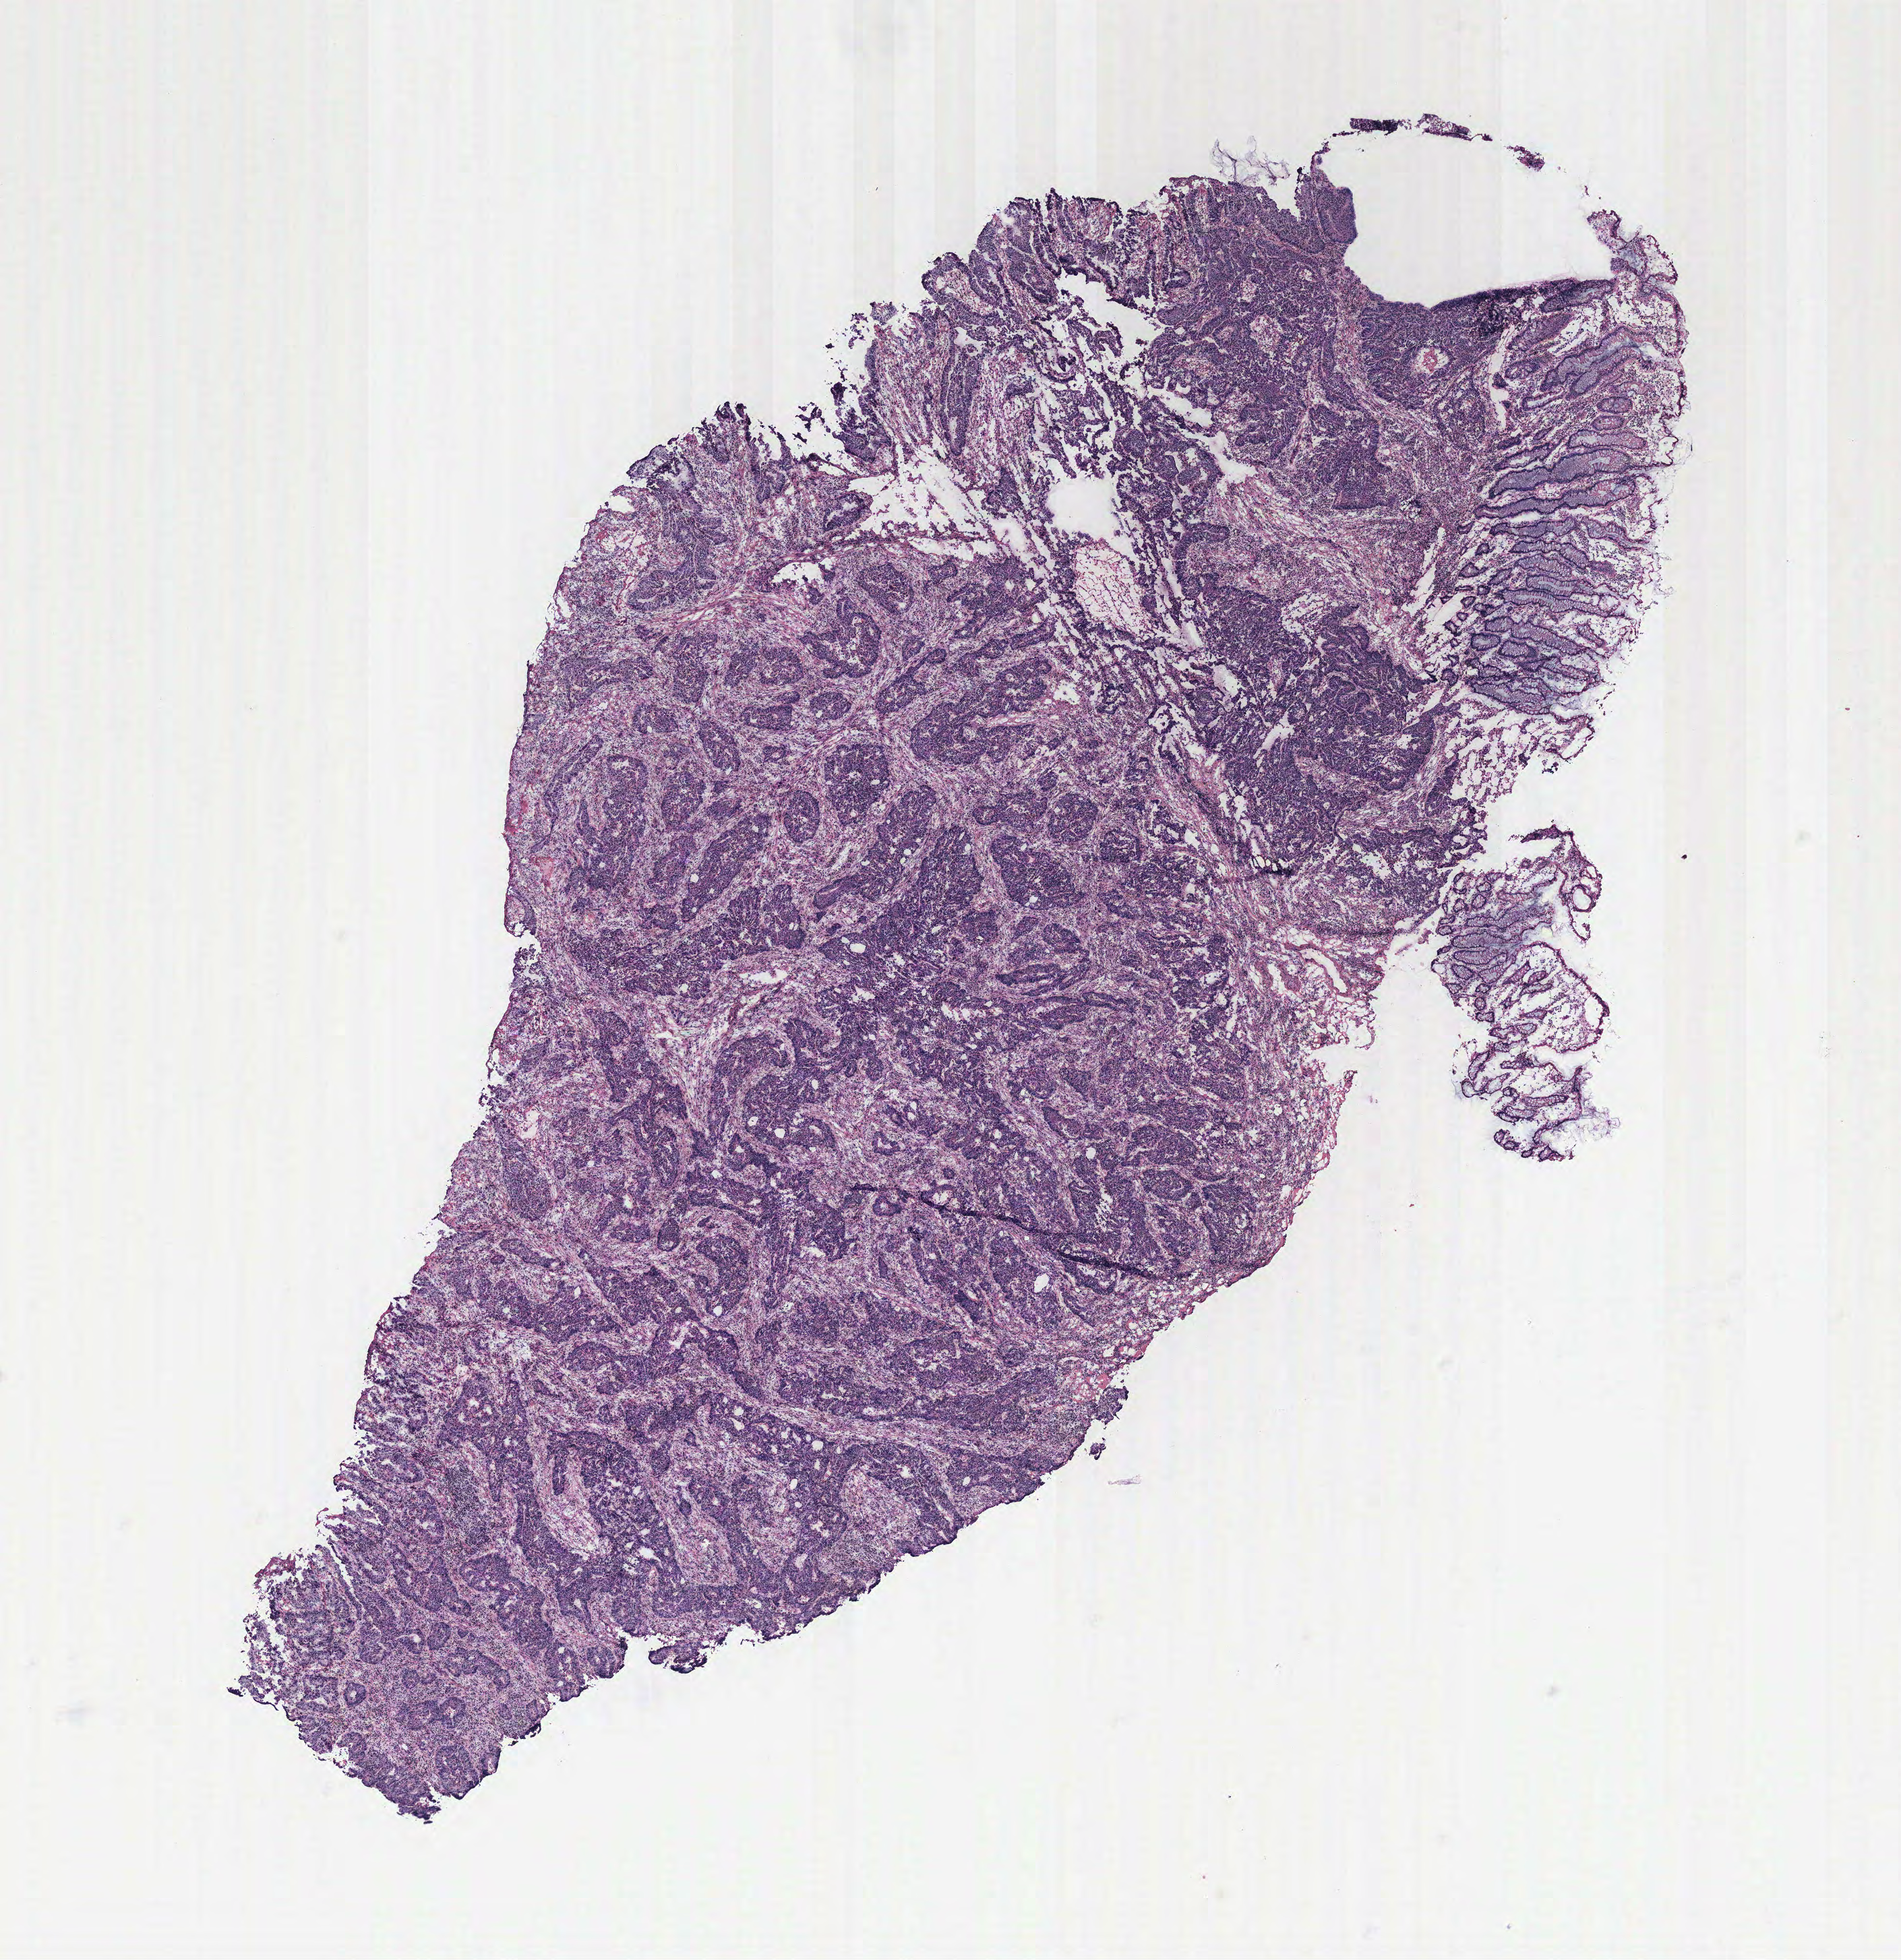
Whole-slide histology image, H&E-stained — a low-resolution overview of the entire scanned area, about 11.3 x 11.6 mm (slide scanned at 40x); colon, normal (non-tumour) tissue. Patient: male, age 87 years.
This section: normal (non-tumour) tissue from the same patient. Patient diagnosis: Adenocarcinoma, NOS.